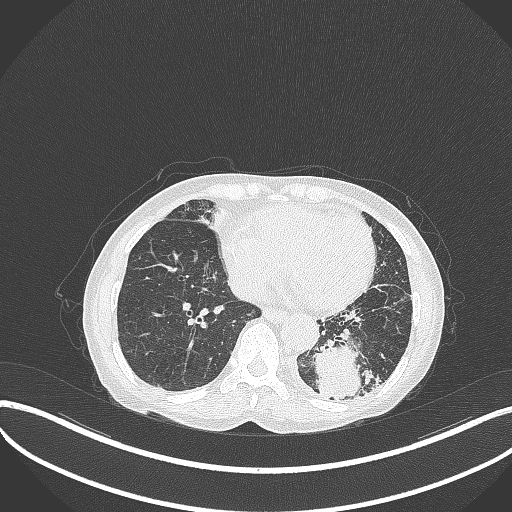
Chest CT, one axial slice. Slice 94 of 370 in the series (ordered by position). Reconstruction kernel B70f. 120 kVp. Lung window (W 1500 / L -600 HU). 512 × 512 image matrix. Female patient, age 78 years. From the clinical record (not read from this slice): clinical TNM (as recorded): T3 N0 M1.
Annotated regions visible in this slice (rectangle marked by the reading radiologist):
- lung tumour (recorded histology: squamous cell carcinoma): bounding box <312,336,369,402> (left, top, right, bottom; pixels)